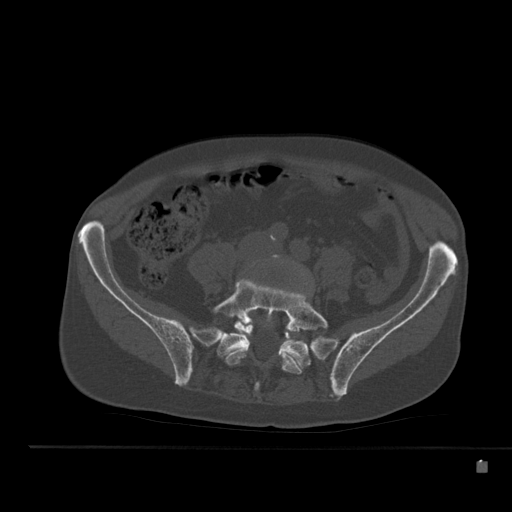
CT including the spine, one axial slice; slice 123 of 517 in the series (ordered by position); reconstruction kernel Br40s; 120 kVp; bone window (W 1800 / L 400 HU); 1.5 mm slice thickness; 512 × 512 image matrix, field of view 408 × 408 mm. Patient: male, 70 years. Case-level facts recorded for this patient, not image findings: primary cancer: renal; vertebrae with lytic lesions (as recorded): T4, T6, T10, T12, L3, L4, L5.
Structures marked on this image (semi-automatically segmented with operator editing):
- L4 vertebra: box from (x=272, y=254) to (x=309, y=278) px
- L5 vertebra: (x=211, y=279)–(x=329, y=392)